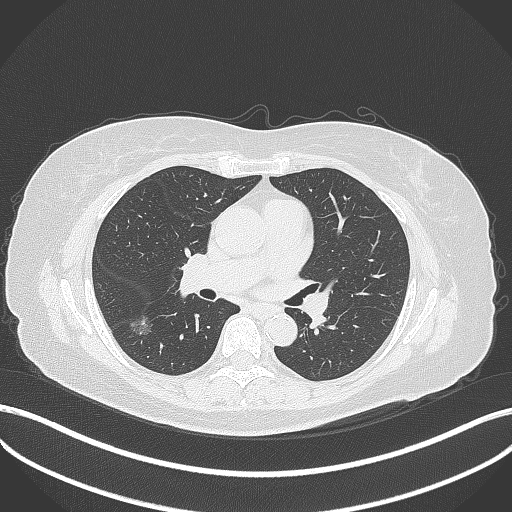
Chest CT, one axial slice; slice 176 of 322 in the series (ordered by position); lung window (W 1500 / L -600 HU); 1 mm slice thickness; 512 × 512 image matrix, field of view 400 × 400 mm. Patient: female, 64 years. From the clinical record (not read from this slice): clinical TNM (as recorded): T1c N0 M0.
Outlined on this slice (rectangle marked by the reading radiologist):
- lung tumour (recorded histology: adenocarcinoma): bounding box <126,312,156,340> (left, top, right, bottom; pixels)